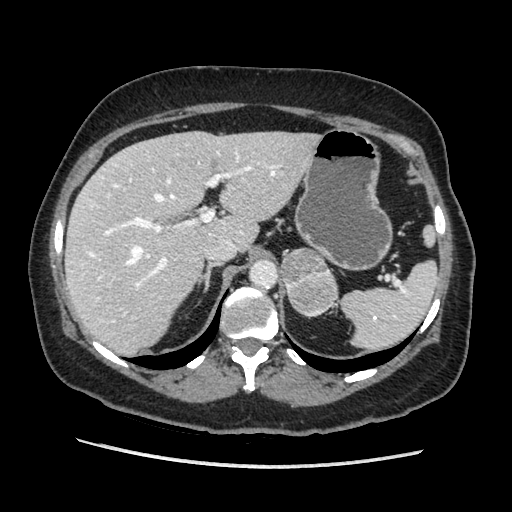
Contrast-enhanced abdominal CT, one axial slice; position 136 of 203 along the scan axis; soft-tissue window (W 400 / L 40 HU); 1.25 mm slice thickness; 512 × 512 image matrix, field of view 360 × 360 mm. Female patient. From the clinical record (not read from this slice): diagnosis: adrenocortical carcinoma; tumour side: left adrenal; tumour size at pathology: 6.5 cm; Ki-67 index: 22 %; stage (as recorded): 2.
Outlined on this slice (semi-automatically segmented with operator editing):
- mass: bounding box [x1, y1, x2, y2] px = [281, 249, 336, 314]